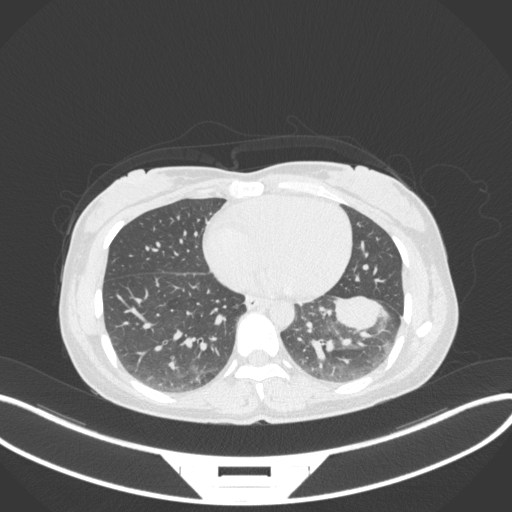
Chest CT, one axial slice. Slice 135 of 361 in the series (ordered by position). Reconstruction kernel B31f. 120 kVp. Lung window (W 1500 / L -600 HU). 1 mm slice thickness. 512 × 512 image matrix, field of view 400 × 400 mm. Patient: female, 41 years. From the clinical record (not read from this slice): clinical TNM (as recorded): T2a N3 M1b.
Annotated regions visible in this slice (bounding box drawn by a radiologist):
- lung tumour (recorded histology: adenocarcinoma): bounding box (x1, y1, x2, y2) in pixels: (328, 296, 390, 336)